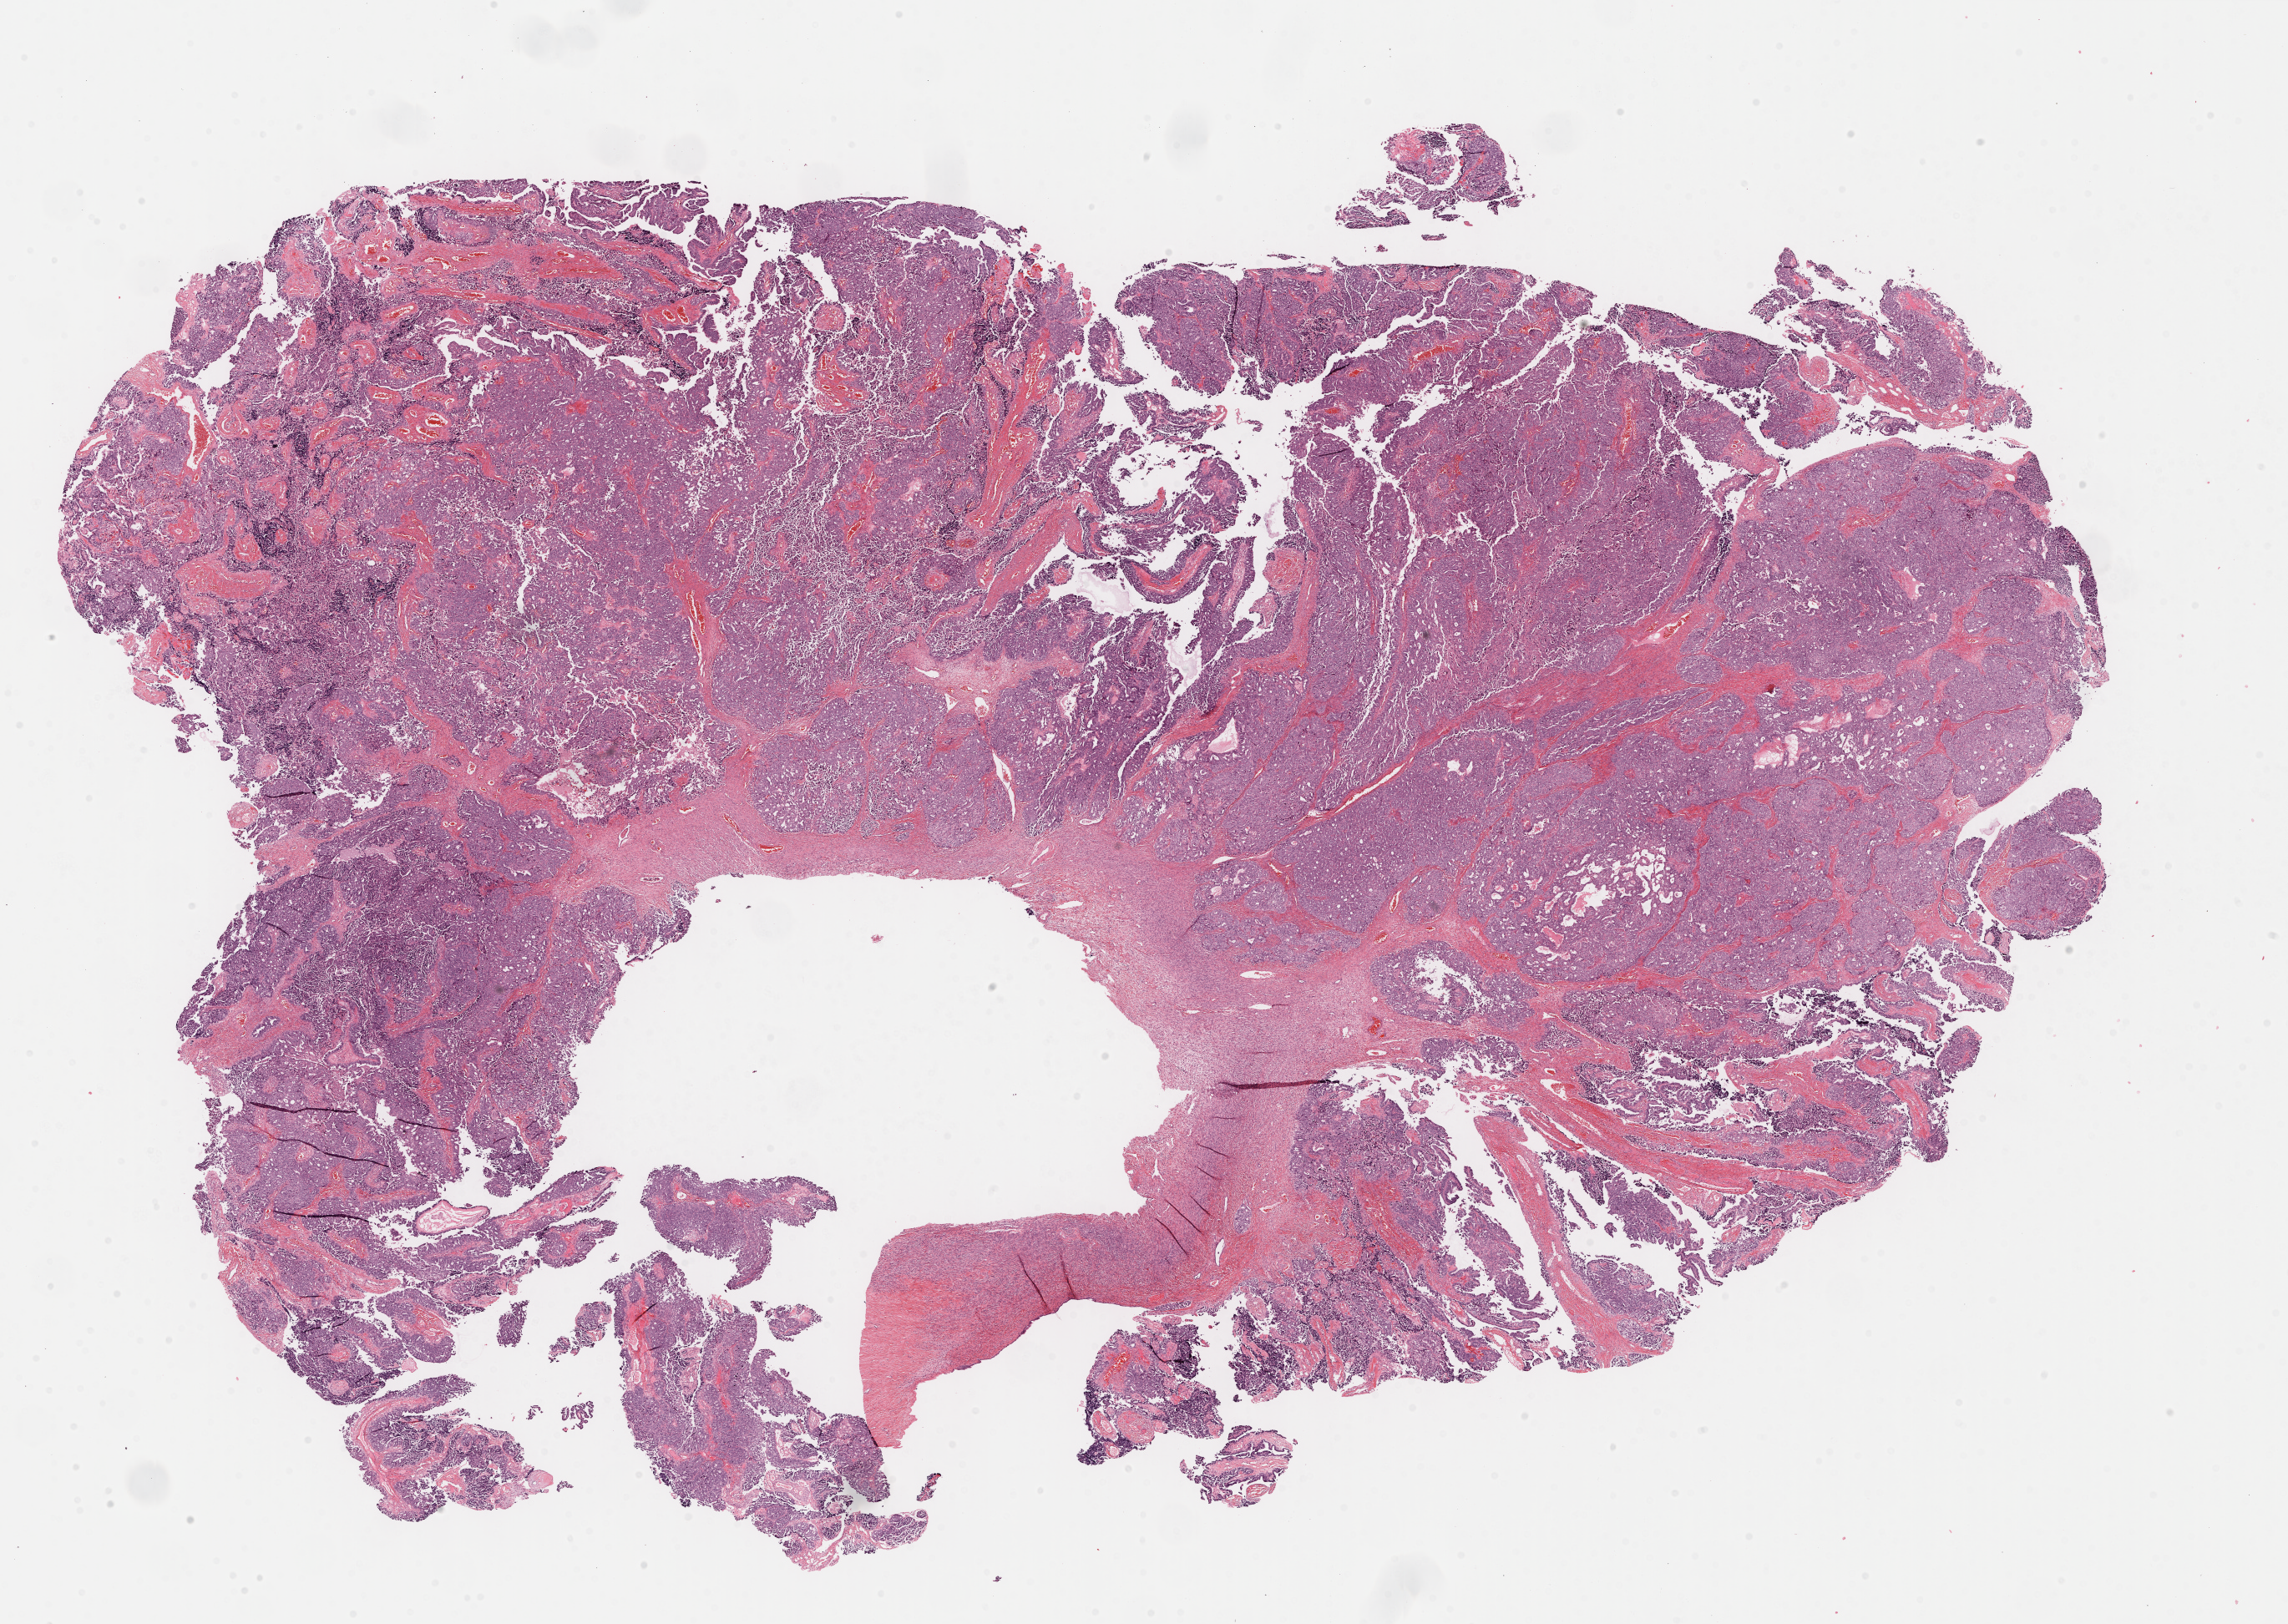
Digitized H&E-stained tissue section (whole slide) — a low-resolution overview of the entire scanned area, about 22.1 x 15.7 mm (acquisition: 40x scan). FFPE section. Ovary, primary tumour sample. Female, age 59 years at initial diagnosis. Histologic grade: G3 (poorly differentiated).
FIGO stage: IIIC. Pathologic diagnosis: Serous cystadenocarcinoma, NOS.